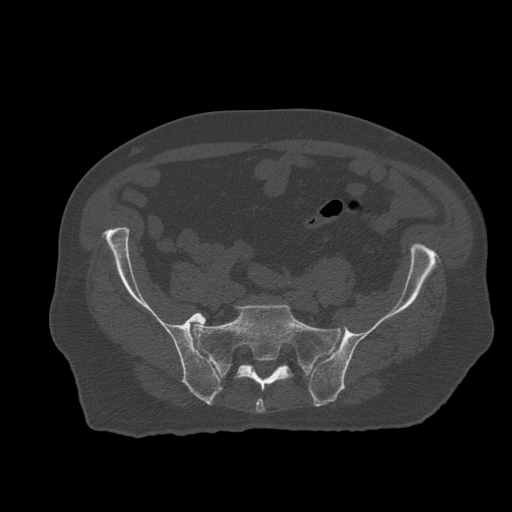
CT including the spine, one axial slice; reconstruction kernel STANDARD; 120 kVp; bone window (W 1800 / L 400 HU); 512 × 512 image matrix. Patient age 73 years. From the clinical record (not read from this slice): primary cancer: prostate; vertebrae with lytic lesions (as recorded): L2.
Outlined on this slice (semi-automatically segmented with operator editing):
- L5 vertebra: bounding box <213,369,217,375> (left, top, right, bottom; pixels)